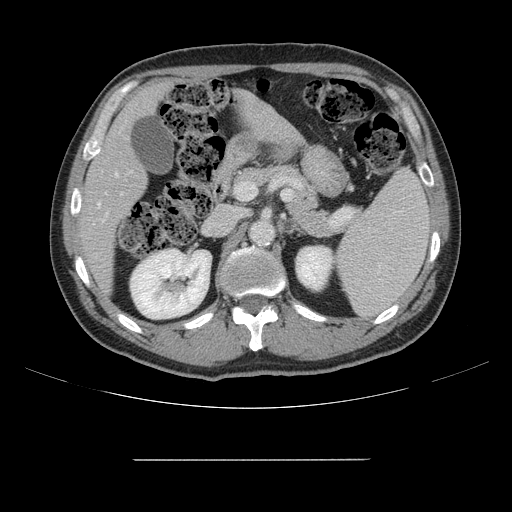
Contrast-enhanced abdominal CT, one axial slice. Position 80 of 164 along the scan axis. 120 kVp. Intravenous contrast given. Soft-tissue window (W 400 / L 40 HU). 2.5 mm slice thickness. 512 × 512 image matrix. Male patient, age 54 years. From the clinical record (not read from this slice): diagnosis: colorectal cancer liver metastases, imaged before liver resection; multiple liver metastases: yes; largest metastasis: 1 cm; chemotherapy before resection: yes.
Outlined on this slice (outlined manually by an expert reader):
- hepatic veins: box from (x=97, y=173) to (x=118, y=207) px
- liver: (x=83, y=87)–(x=295, y=288)
- planned liver remnant (the part of the liver to remain after resection): (x=83, y=87)–(x=163, y=288)
- portal vein (with intrahepatic branches): (x=106, y=193)–(x=122, y=216)